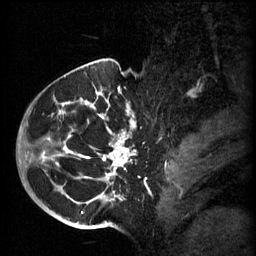
Breast MRI (dynamic contrast-enhanced), one sagittal slice; slice 43 of 60 in the series (ordered by position); 3 images stored at this slice position (order not interpretable as contrast timing); 1.5 T; TE 4.2 ms, TR 11 ms; 2 mm slice thickness; 256 × 256 image matrix, field of view 200 × 200 mm. Patient: female, 51 years.
Annotated regions visible in this slice (semi-automatically segmented with operator editing):
- analysis volume of interest (the breast-tissue region the enhancement analysis was run in; not a lesion): bounding box <48,82,158,197> (left, top, right, bottom; pixels)
- tumour enhancement mask (voxels above the 70 % enhancement threshold inside the analysis volume of interest): <48,92,135,197>